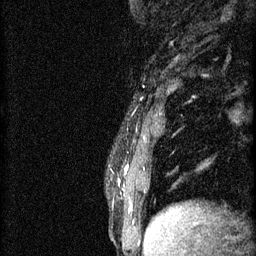
Breast MRI (dynamic contrast-enhanced), one sagittal slice. Slice 13 of 60 in the series (ordered by position). 3 images stored at this slice position (order not interpretable as contrast timing). 1.5 T. TE 4.2 ms, TR 11 ms. 2 mm slice thickness. 256 × 256 image matrix. Patient: female, 37 years.
Annotated regions visible in this slice (semi-automatic segmentation, software-assisted and operator-edited):
- analysis volume of interest (the breast-tissue region the enhancement analysis was run in; not a lesion): box from (x=119, y=142) to (x=171, y=221) px
- tumour enhancement mask (voxels above the 70 % enhancement threshold inside the analysis volume of interest): (x=119, y=166)–(x=128, y=183)